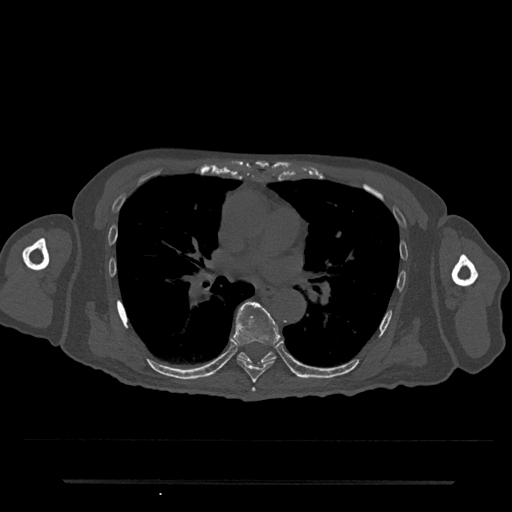
CT including the spine, one axial slice. Position 460 of 797 along the scan axis. Reconstruction kernel Br40s/3. Bone window (W 1800 / L 400 HU). 0.5 mm slice thickness. 512 × 512 image matrix, field of view 427 × 427 mm. Patient: male, 74 years. From the clinical record (not read from this slice): primary cancer: prostate.
Structures marked on this image (semi-automatic segmentation, software-assisted and operator-edited):
- T6 vertebra: bounding box [x1, y1, x2, y2] px = [252, 388, 256, 392]
- T7 vertebra: [233, 301, 281, 383]
- T8 vertebra: [237, 352, 276, 364]